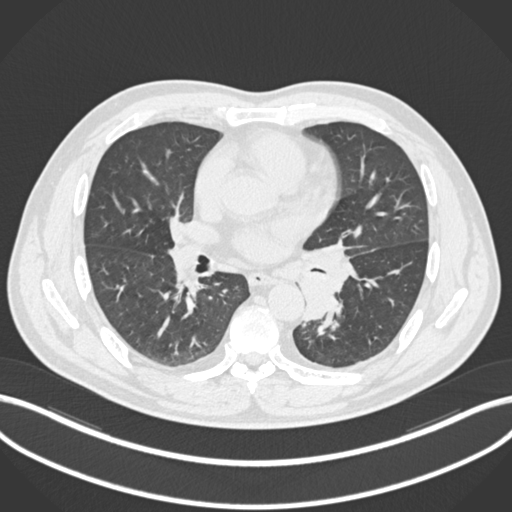
Chest CT, one axial slice. Slice 115 of 223 in the series (ordered by position). Reconstruction kernel B30f. 120 kVp. Lung window (W 1500 / L -600 HU). 1 mm slice thickness. 512 × 512 image matrix, field of view 400 × 400 mm. Male patient, age 50 years. From the clinical record (not read from this slice): clinical TNM (as recorded): T2a N3 M0.
Outlined on this slice (bounding box drawn by a radiologist):
- lung tumour (recorded histology: squamous cell carcinoma): bounding box [x1, y1, x2, y2] px = [296, 244, 359, 326]